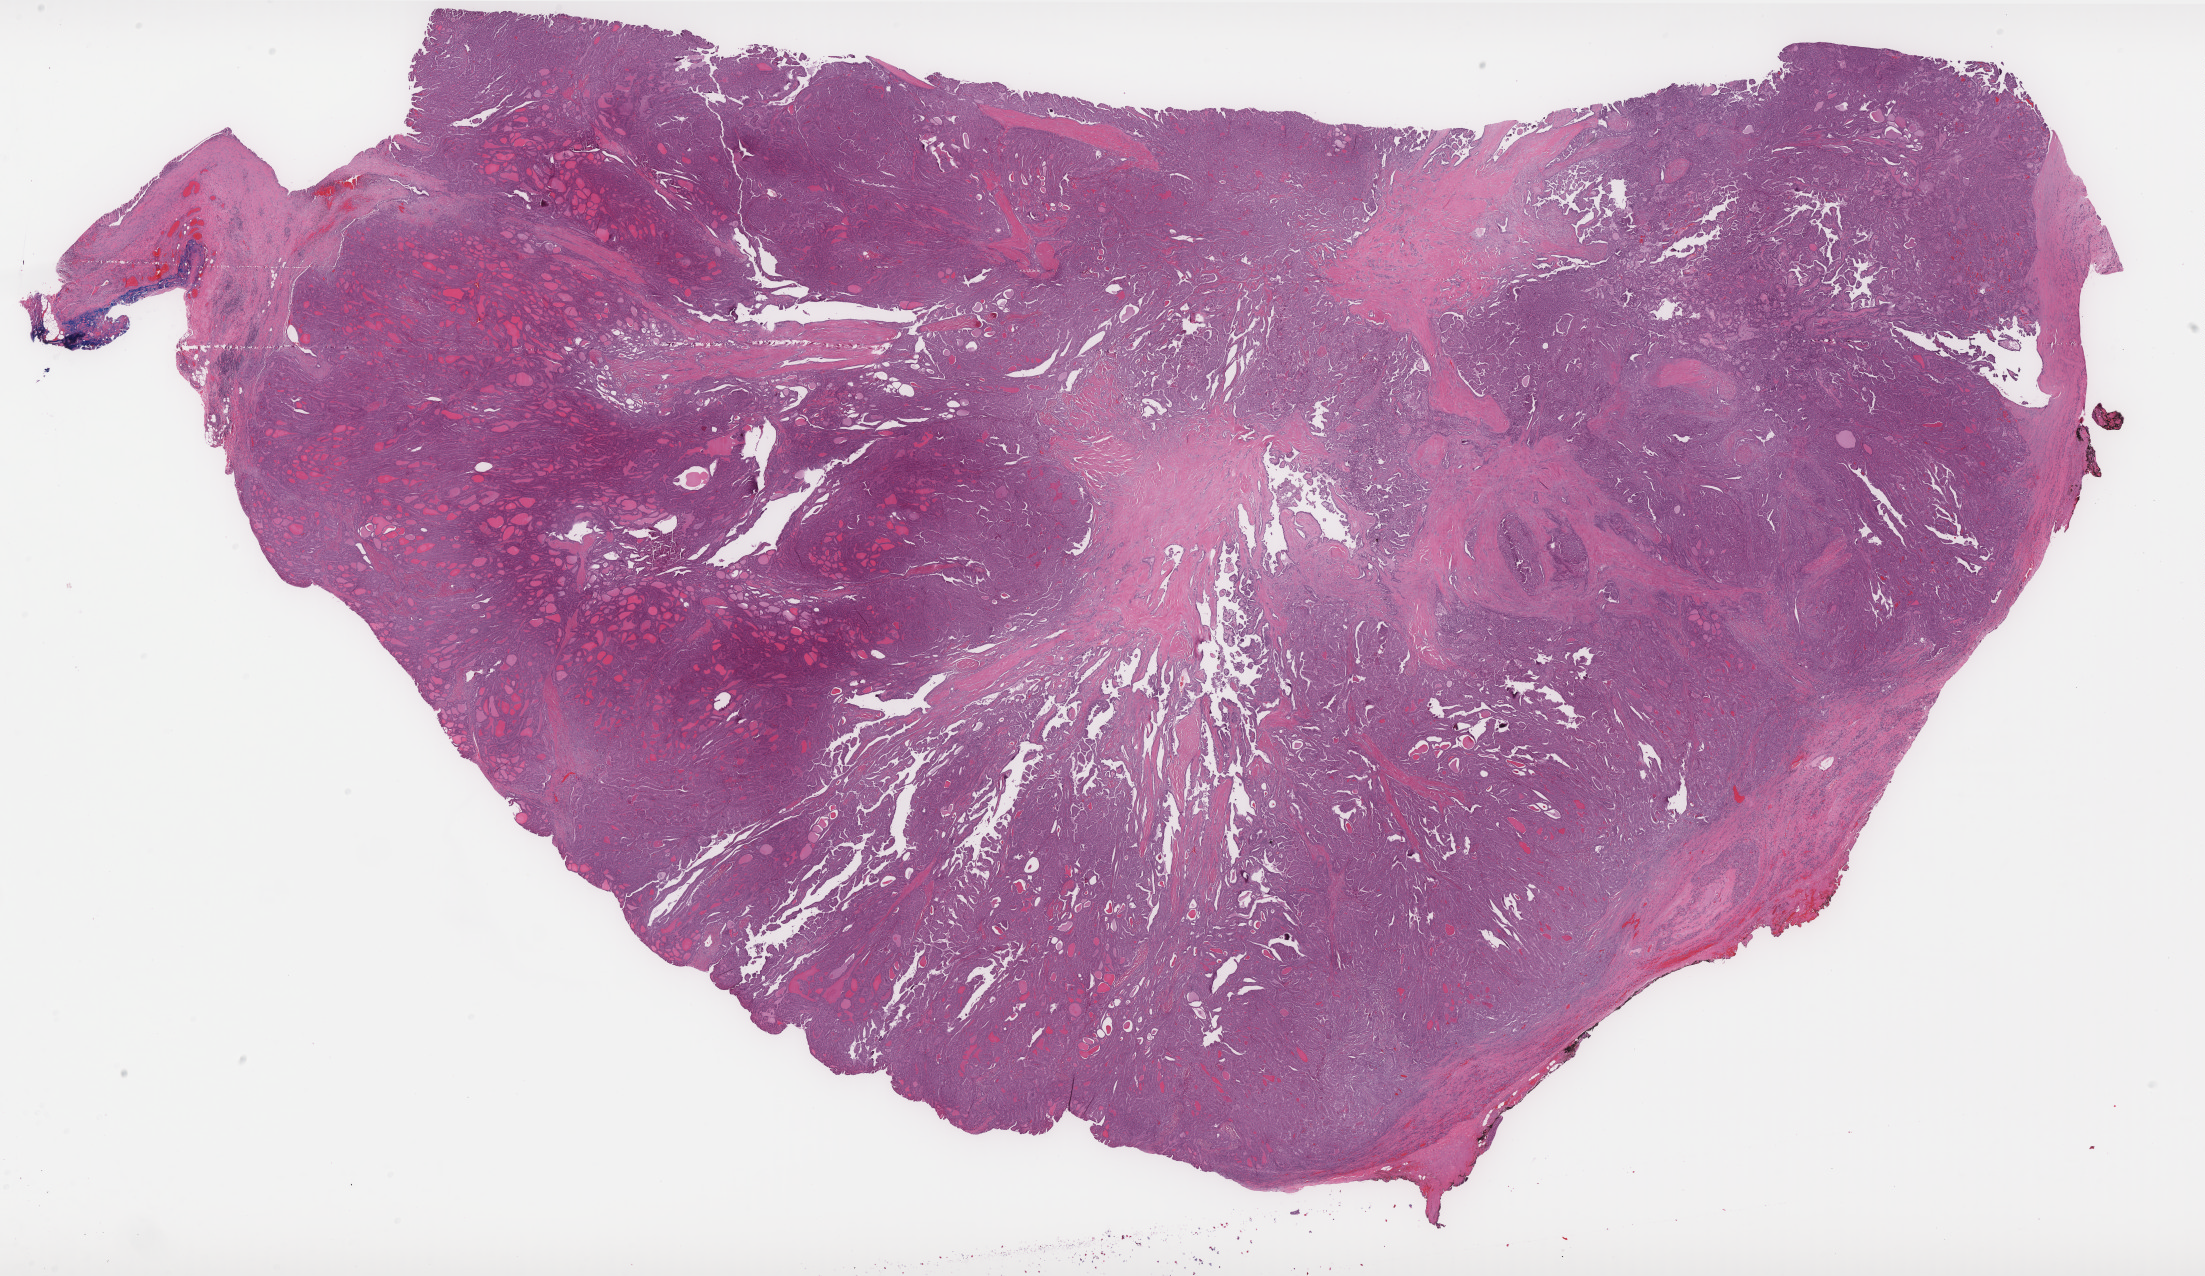
H&E-stained whole-slide image, low-resolution overview of the scanned area, about 35.4 x 20.5 mm (from a 40x scan); FFPE section; thyroid, primary tumour sample. Patient: female, age at initial diagnosis 57 years.
* AJCC pathologic stage: III
* TNM: T3 N1a M0
* lymph nodes positive (case pathology): 7 of 8 examined
* pathologic diagnosis: Papillary carcinoma, columnar cell